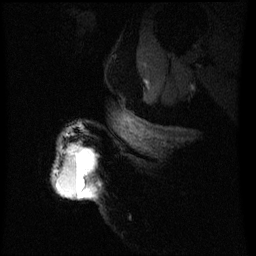
Breast MRI (dynamic contrast-enhanced), one sagittal slice. Slice 48 of 60 in the series (ordered by position). Dynamic contrast-enhanced series, image 2 of 3 at this slice position (ordered by acquisition). 1.5 T. TE 4.2 ms, TR 8 ms. 256 × 256 image matrix. Patient: female, 50 years.
Outlined on this slice (semi-automatic segmentation, software-assisted and operator-edited):
- analysis volume of interest (the breast-tissue region the enhancement analysis was run in; not a lesion): bounding box <54,148,92,199> (left, top, right, bottom; pixels)
- tumour enhancement mask (voxels above the 70 % enhancement threshold inside the analysis volume of interest): <57,150,92,199>